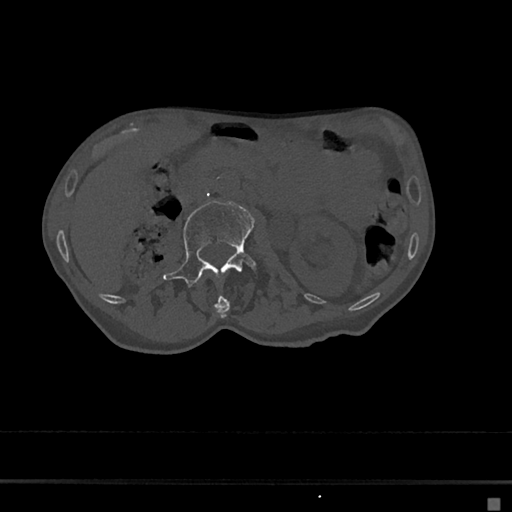
CT including the spine, one axial slice; position 19 of 797 along the scan axis; reconstruction kernel Br40s/3; 120 kVp; bone window (W 1800 / L 400 HU); 512 × 512 image matrix, field of view 360 × 360 mm. Female patient, age 68 years. From the clinical record (not read from this slice): primary cancer: renal.
Outlined on this slice (semi-automatically segmented with operator editing):
- L1 vertebra: bounding box (x1, y1, x2, y2) in pixels: (213, 295, 229, 319)
- L2 vertebra: (163, 201, 259, 290)